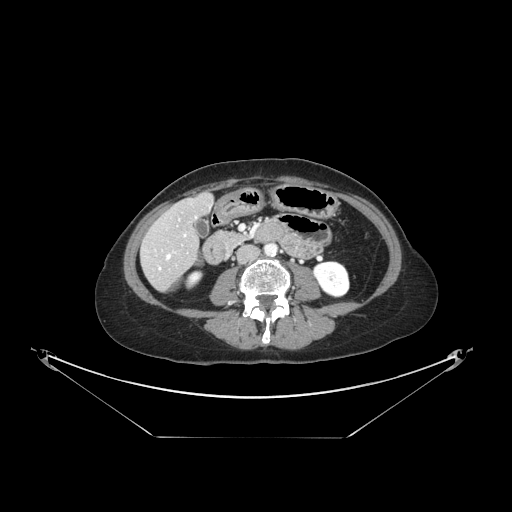
Contrast-enhanced abdominal CT, one axial slice. Slice 42 of 148 in the series (ordered by position). Intravenous contrast given. Soft-tissue window (W 400 / L 40 HU). 2.5 mm slice thickness. 512 × 512 image matrix. Female patient, age 73 years. Case-level facts recorded for this patient, not image findings: diagnosis: colorectal cancer liver metastases, imaged before liver resection; multiple liver metastases: no; largest metastasis: 1 cm; disease in both lobes: no.
Outlined on this slice (outlined manually by an expert reader):
- hepatic veins: box from (x=159, y=234) to (x=186, y=270) px
- liver: (x=143, y=196)–(x=213, y=290)
- planned liver remnant (the part of the liver to remain after resection): (x=161, y=196)–(x=213, y=242)